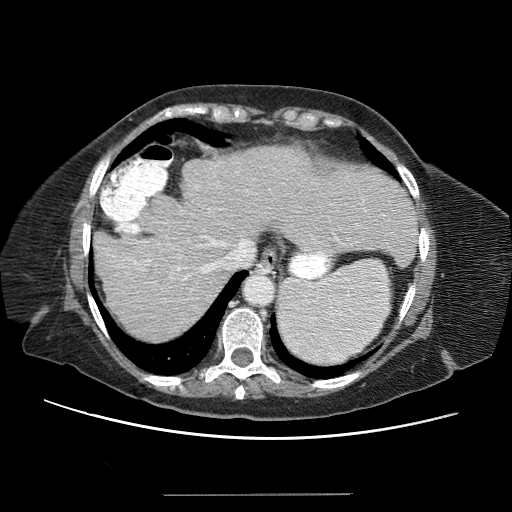
Contrast-enhanced abdominal CT (liver protocol), one axial slice. Slice 49 of 65 in the series (ordered by position). Reconstruction kernel STANDARD. 120 kVp. Soft-tissue window (W 400 / L 40 HU). 2.5 mm slice thickness. 512 × 512 image matrix, field of view 380 × 380 mm. Case-level facts recorded for this patient, not image findings: diagnosis: hepatocellular carcinoma (patient treated with transarterial chemoembolisation; whether this scan precedes or follows treatment is not stated here); TNM stage (as recorded): Stage-IIIB; Child-Pugh class: A; tumour differentiation: moderately differentiated.
Structures marked on this image (semi-automatic segmentation, software-assisted and operator-edited):
- liver parenchyma outside the tumour (the mass and vessels are separate outlines, so this box may not span the whole liver): bounding box [x1, y1, x2, y2] px = [94, 148, 418, 336]
- mass: [138, 241, 186, 284]
- liver vessels: [100, 178, 414, 306]